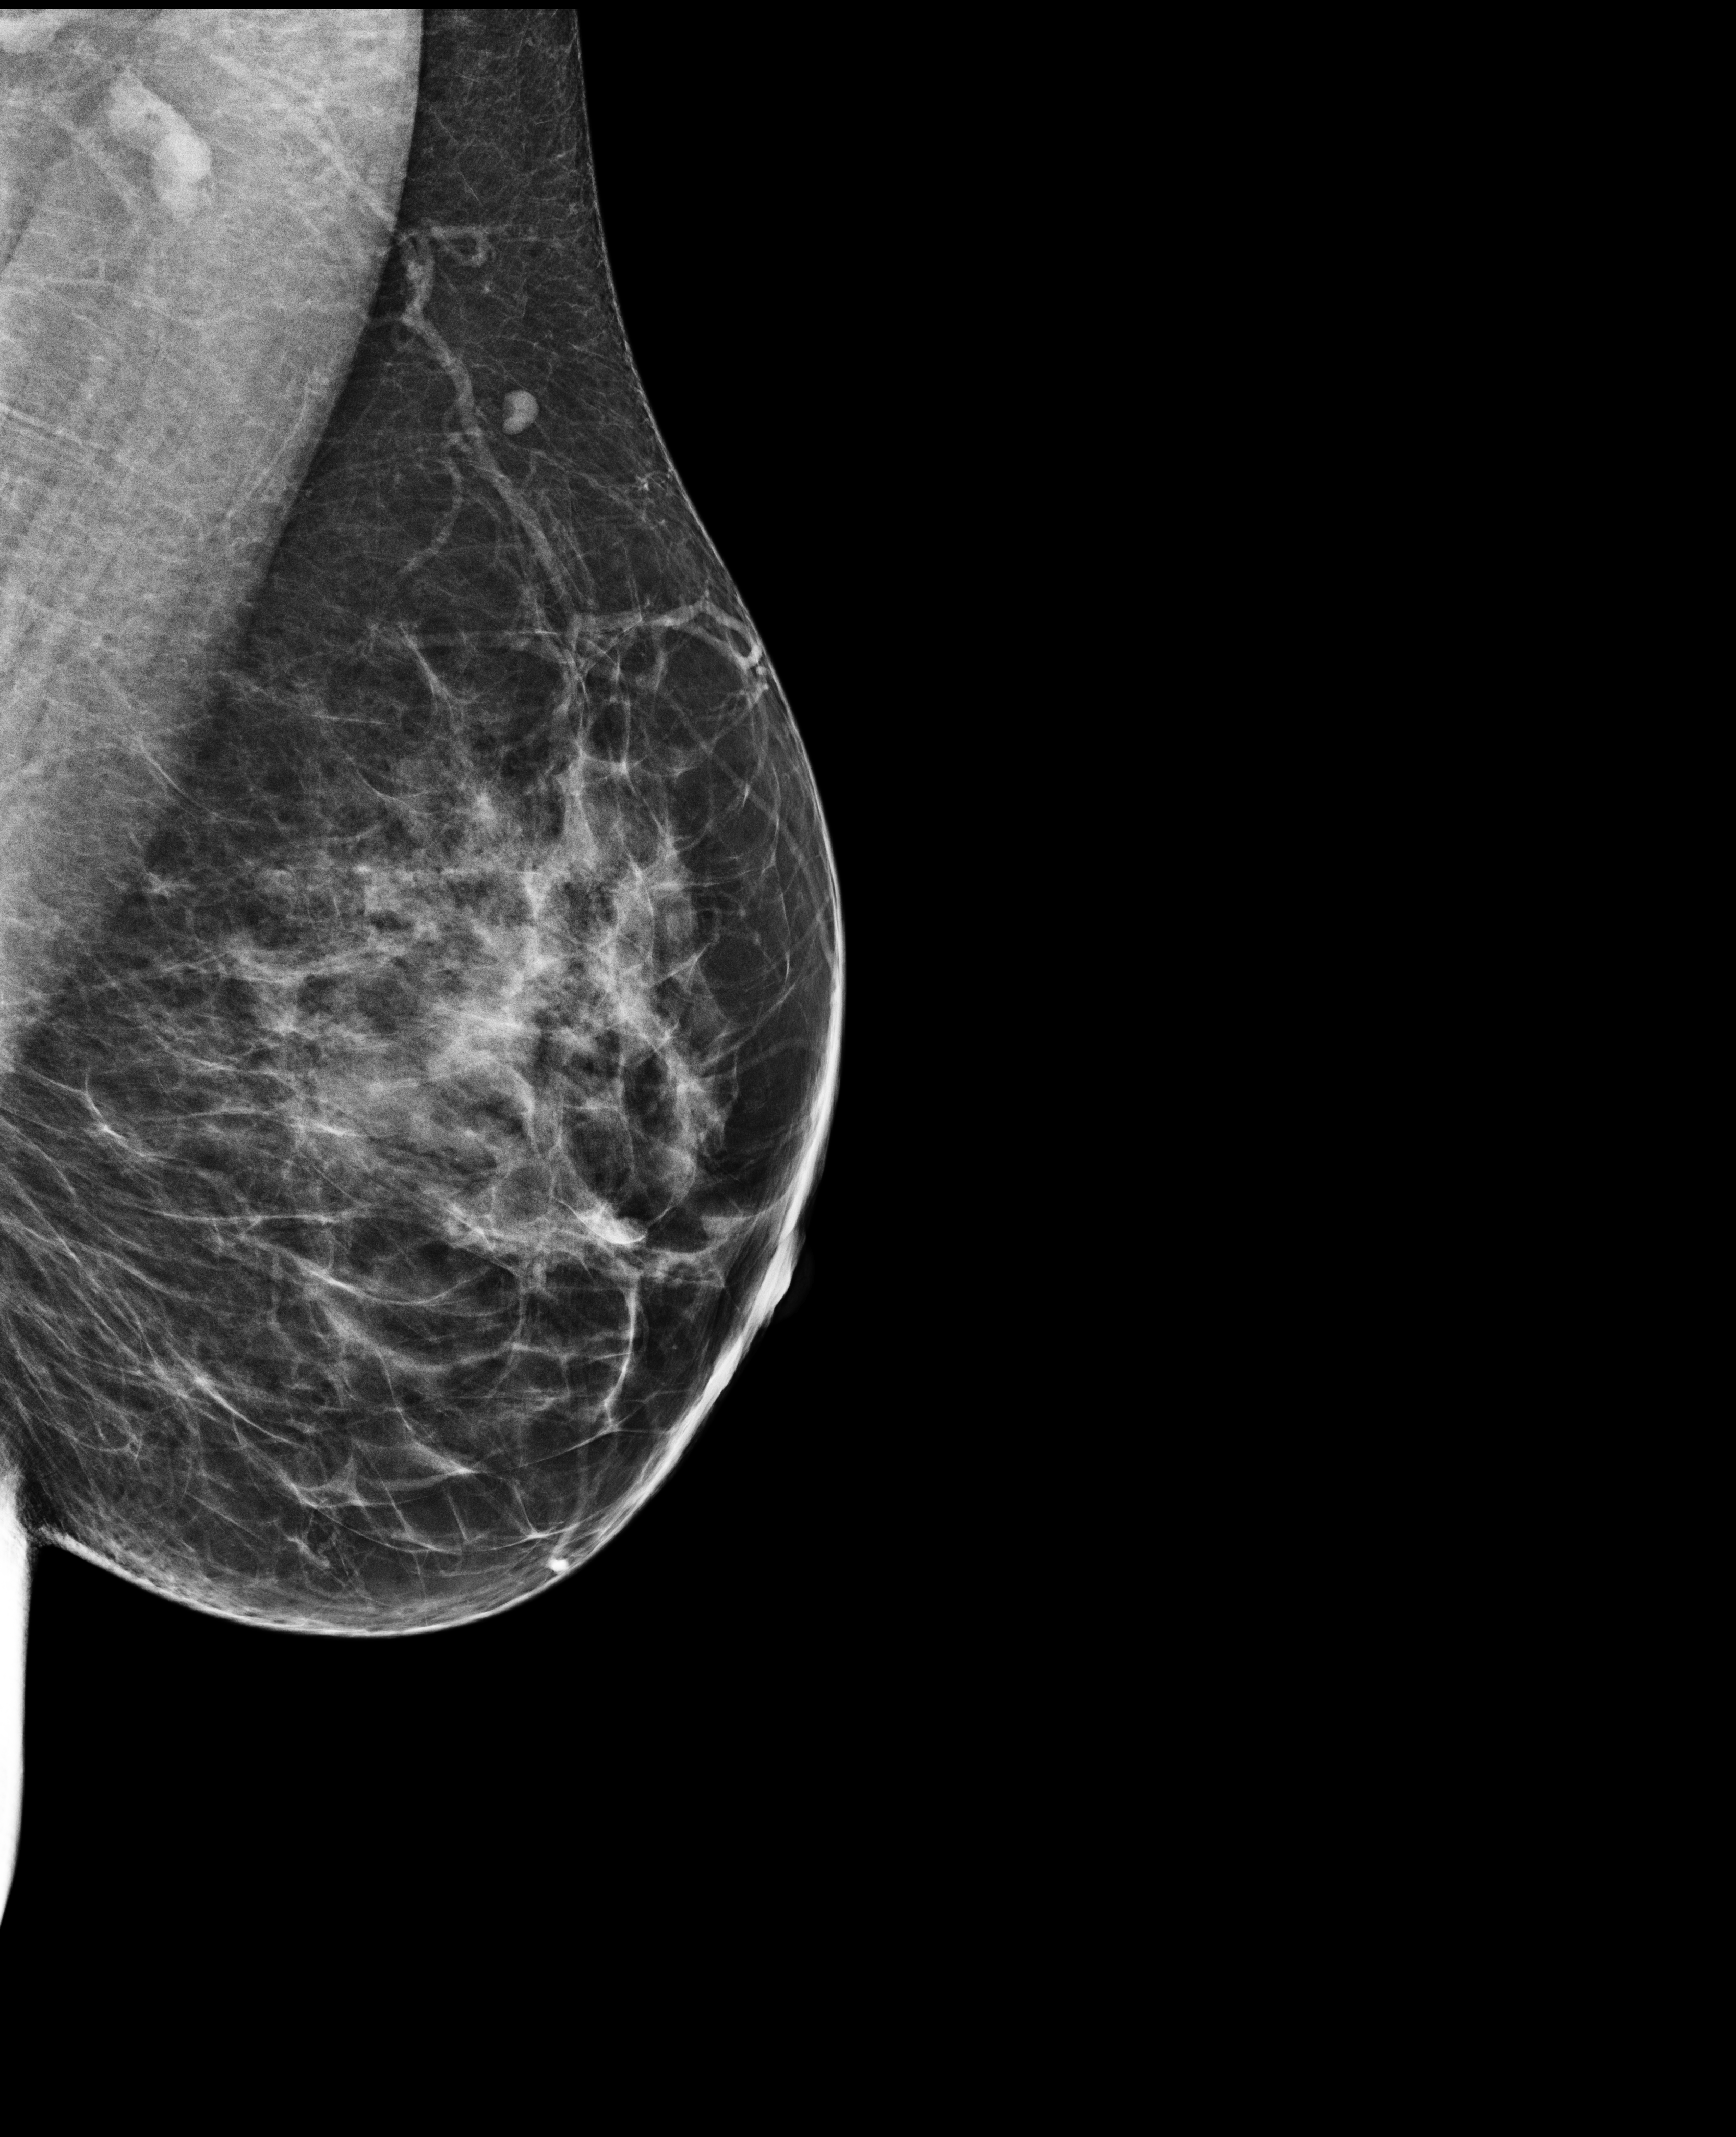
Annual screening mammography examination. Female patient, age 43 years.
Image type: full-field digital mammogram. Breast: left. Projection: MLO view.